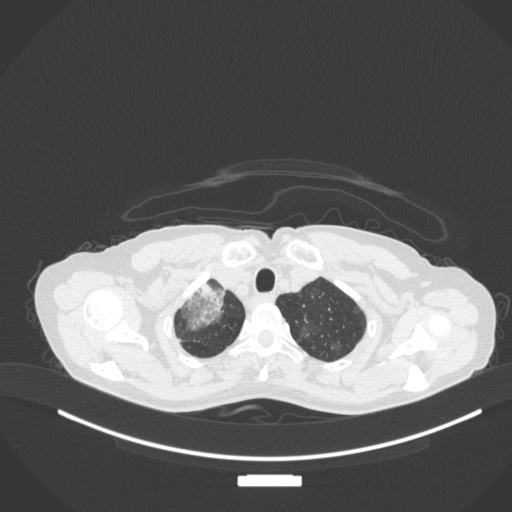
Chest CT, one axial slice. Position 293 of 311 along the scan axis. Lung window (W 1500 / L -600 HU). 512 × 512 image matrix, field of view 400 × 400 mm. Patient: female, 59 years. Case-level facts recorded for this patient, not image findings: clinical TNM (as recorded): T3 N0 M0; histopathological grade: G1.
Outlined on this slice (rectangle marked by the reading radiologist):
- lung tumour (recorded histology: adenocarcinoma): bounding box <176,277,229,332> (left, top, right, bottom; pixels)